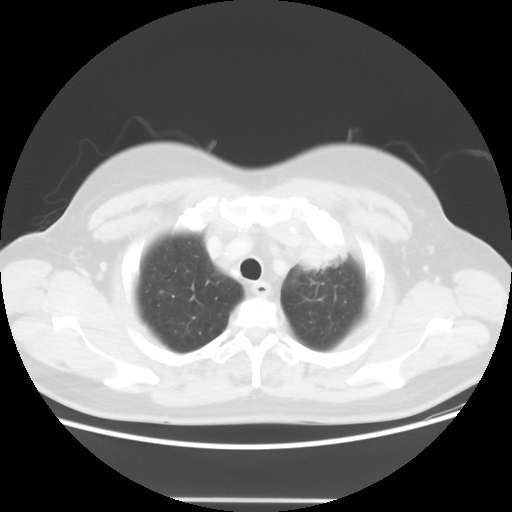
Chest CT, one axial slice. Slice 46 of 52 in the series (ordered by position). 120 kVp. Lung window (W 1500 / L -600 HU). 5 mm slice thickness. 512 × 512 image matrix. Female patient, age 52 years. From the clinical record (not read from this slice): clinical TNM (as recorded): T2 N3 M0.
Annotated regions visible in this slice (rectangle marked by the reading radiologist):
- lung tumour (recorded histology: adenocarcinoma): bounding box [x1, y1, x2, y2] px = [291, 224, 355, 272]